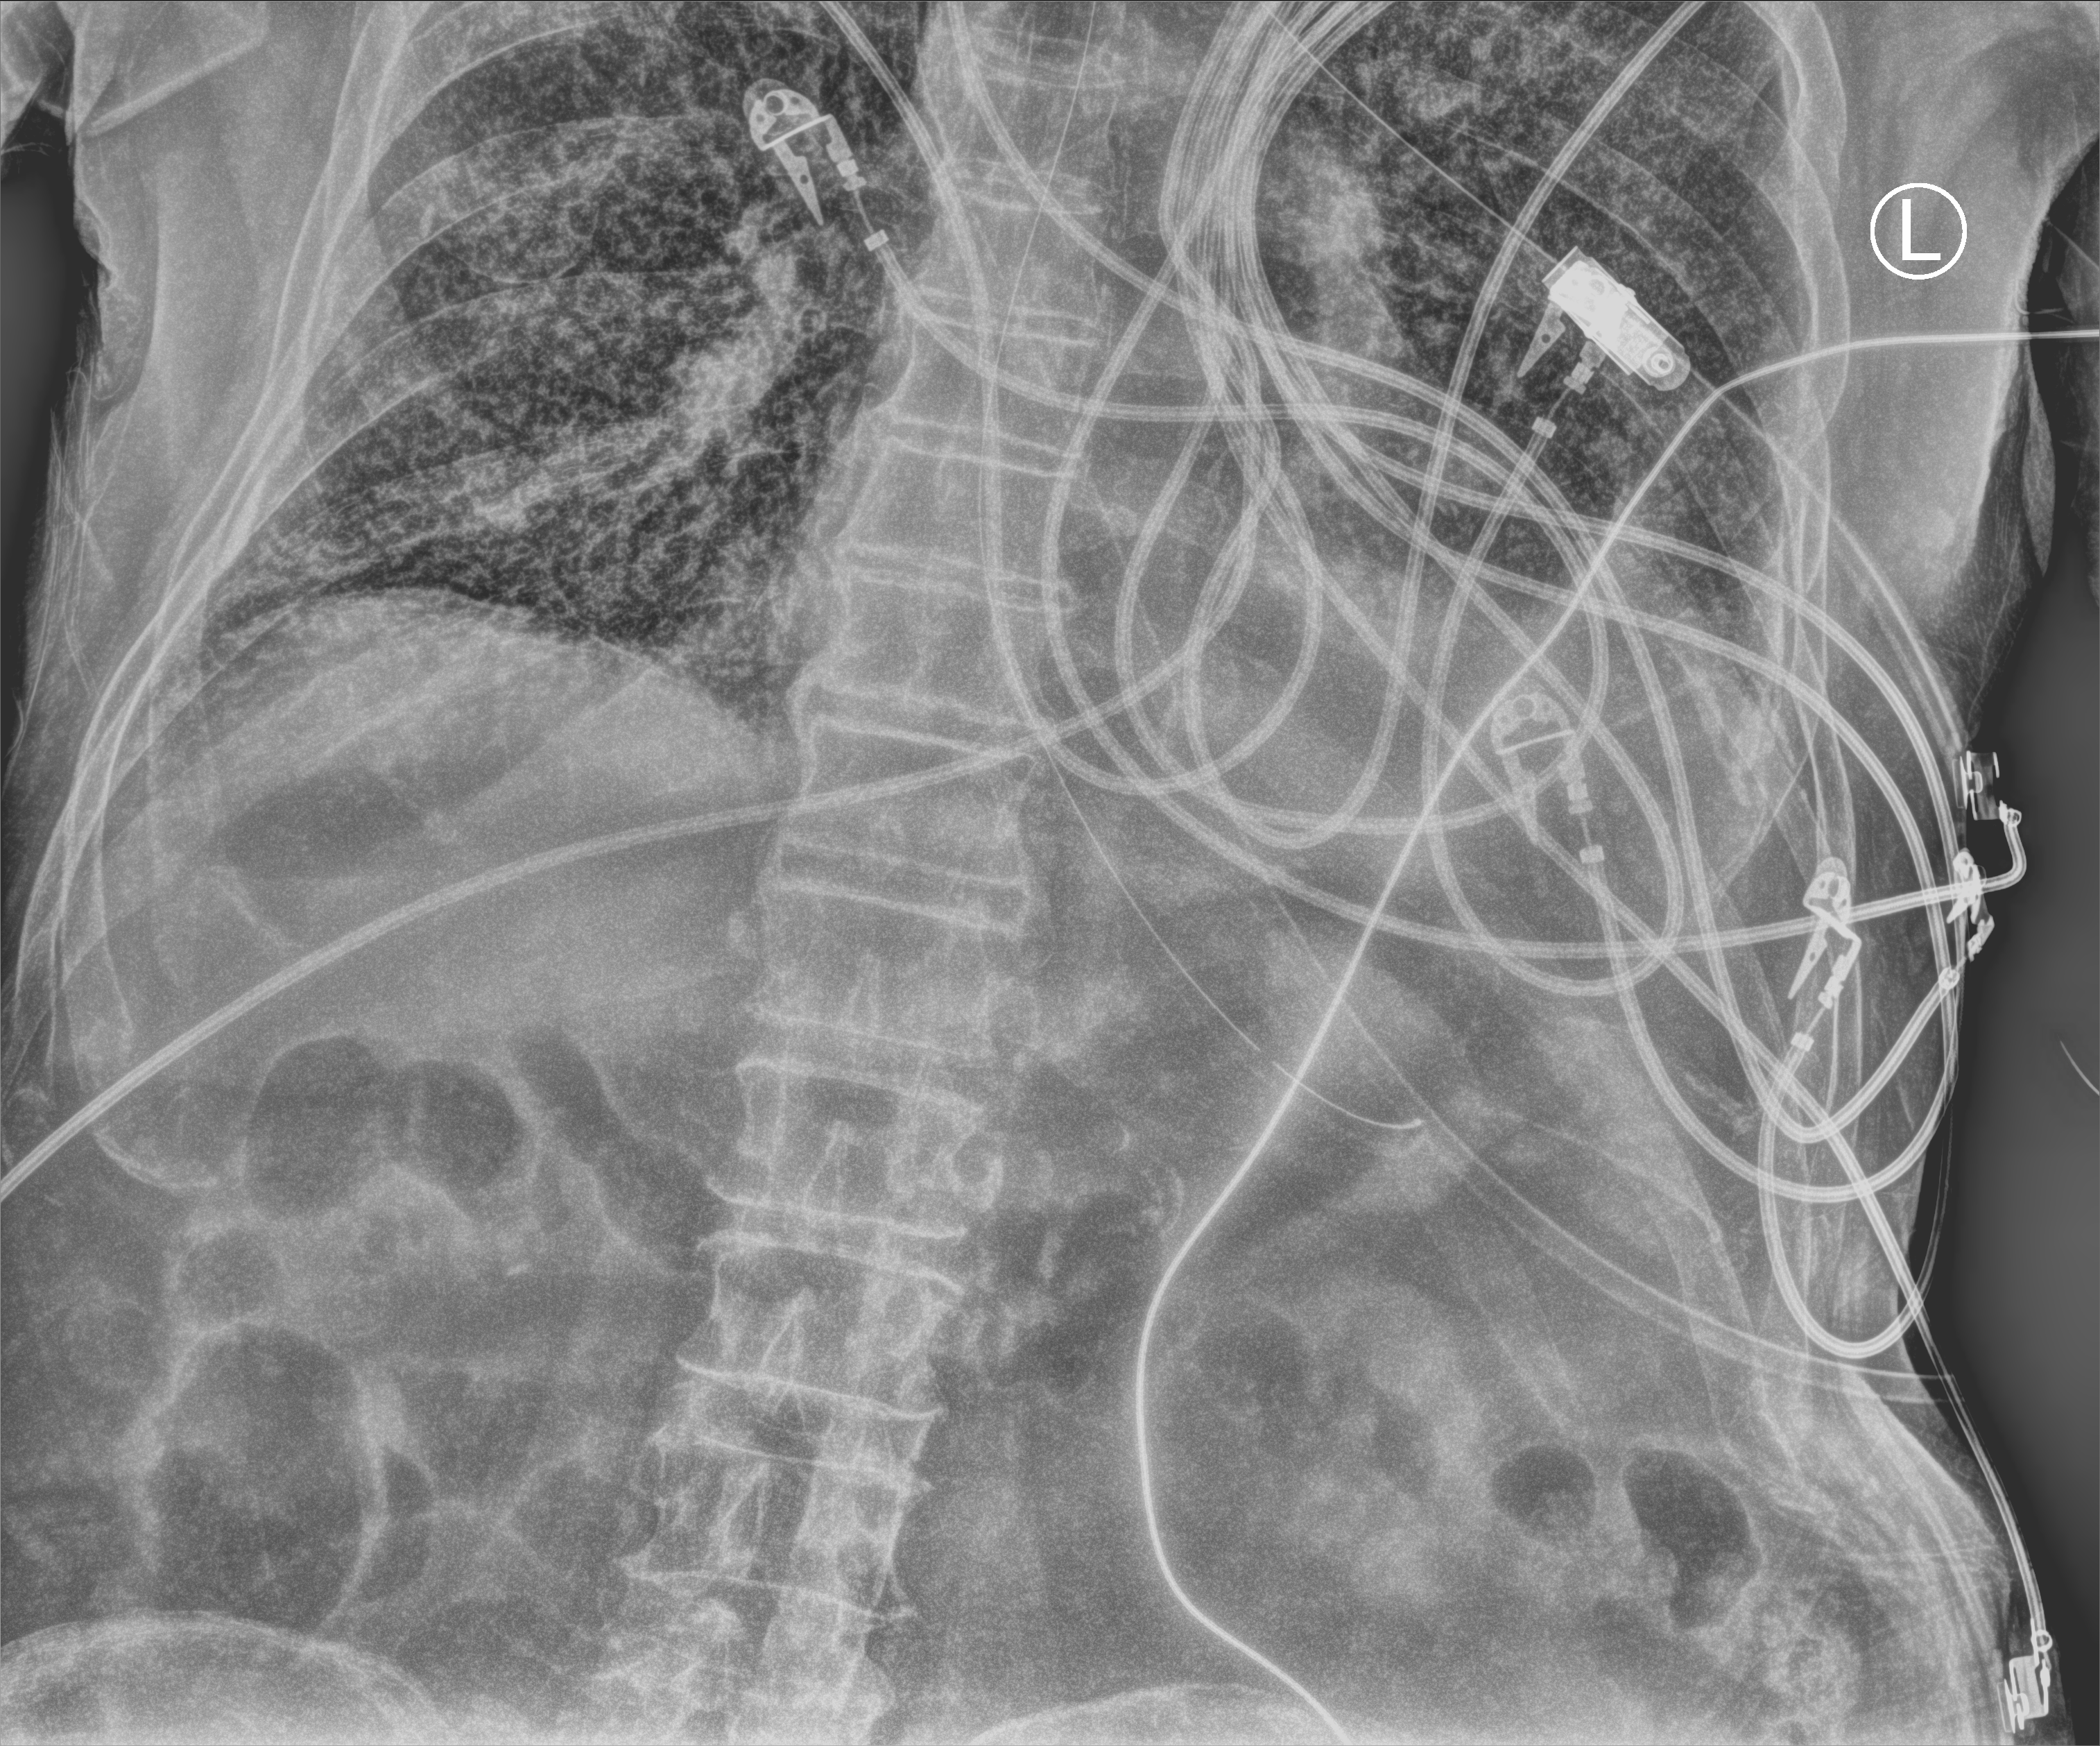
Chest X-ray (portable); anteroposterior (AP) projection. Male patient hospitalised with COVID-19, age 75–90 years.
From the hospital-stay record, not from the radiograph (when in the stay this image was taken is not recorded): admitted to intensive care during this hospital stay: yes; mechanically ventilated during this hospital stay: yes; length of hospital stay: 6 days.